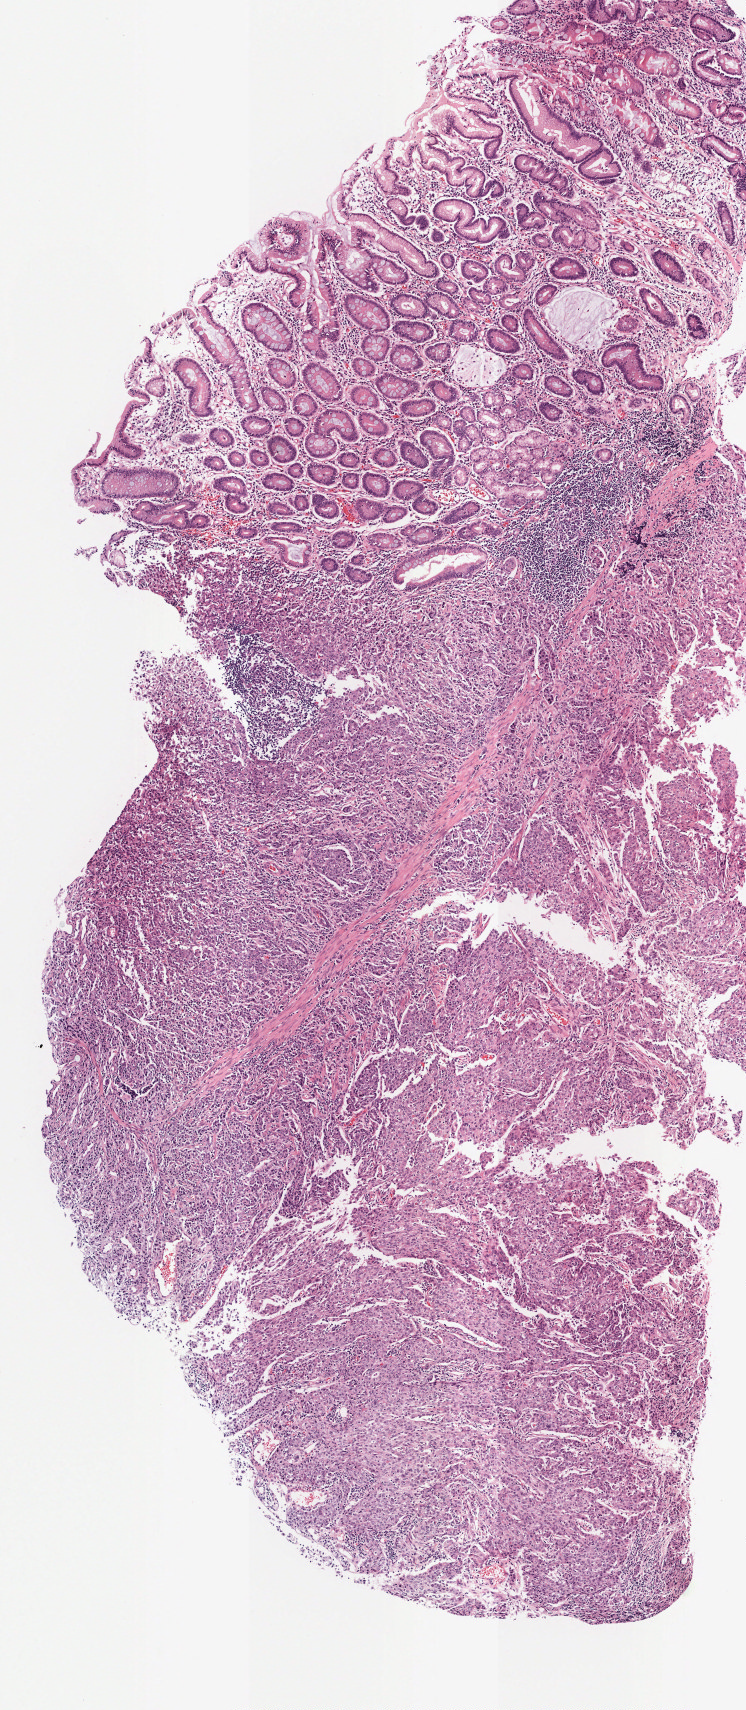
Whole-slide histology image, H&E-stained, shown as a low-resolution overview of the whole scanned area (about 2.9 x 6.8 mm); formalin-fixed paraffin-embedded (FFPE) diagnostic section; sample: primary tumour, stomach. Male, age 68 years at initial diagnosis. Histologic grade: G3 (poorly differentiated).
Histologic diagnosis: Carcinoma, diffuse type (gastric antrum). AJCC pathologic stage: IIB.